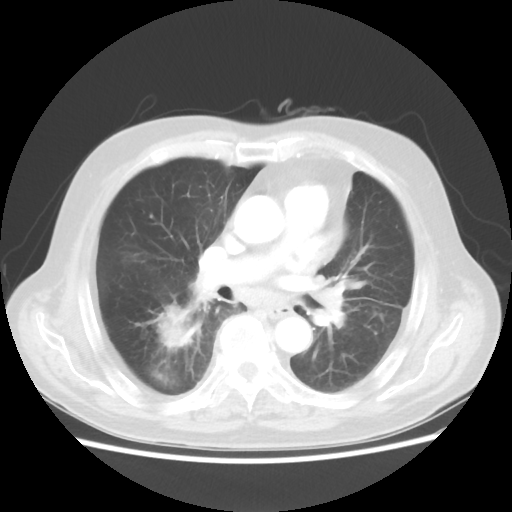
Chest CT, one axial slice. 100 kVp. Lung window (W 1500 / L -600 HU). 5 mm slice thickness. 512 × 512 image matrix, field of view 359 × 359 mm. Patient: male, 83 years. From the clinical record (not read from this slice): clinical TNM (as recorded): T2 N3 M0.
Annotated regions visible in this slice (bounding box drawn by a radiologist):
- lung tumour (recorded histology: adenocarcinoma): box from (x=144, y=289) to (x=198, y=366) px